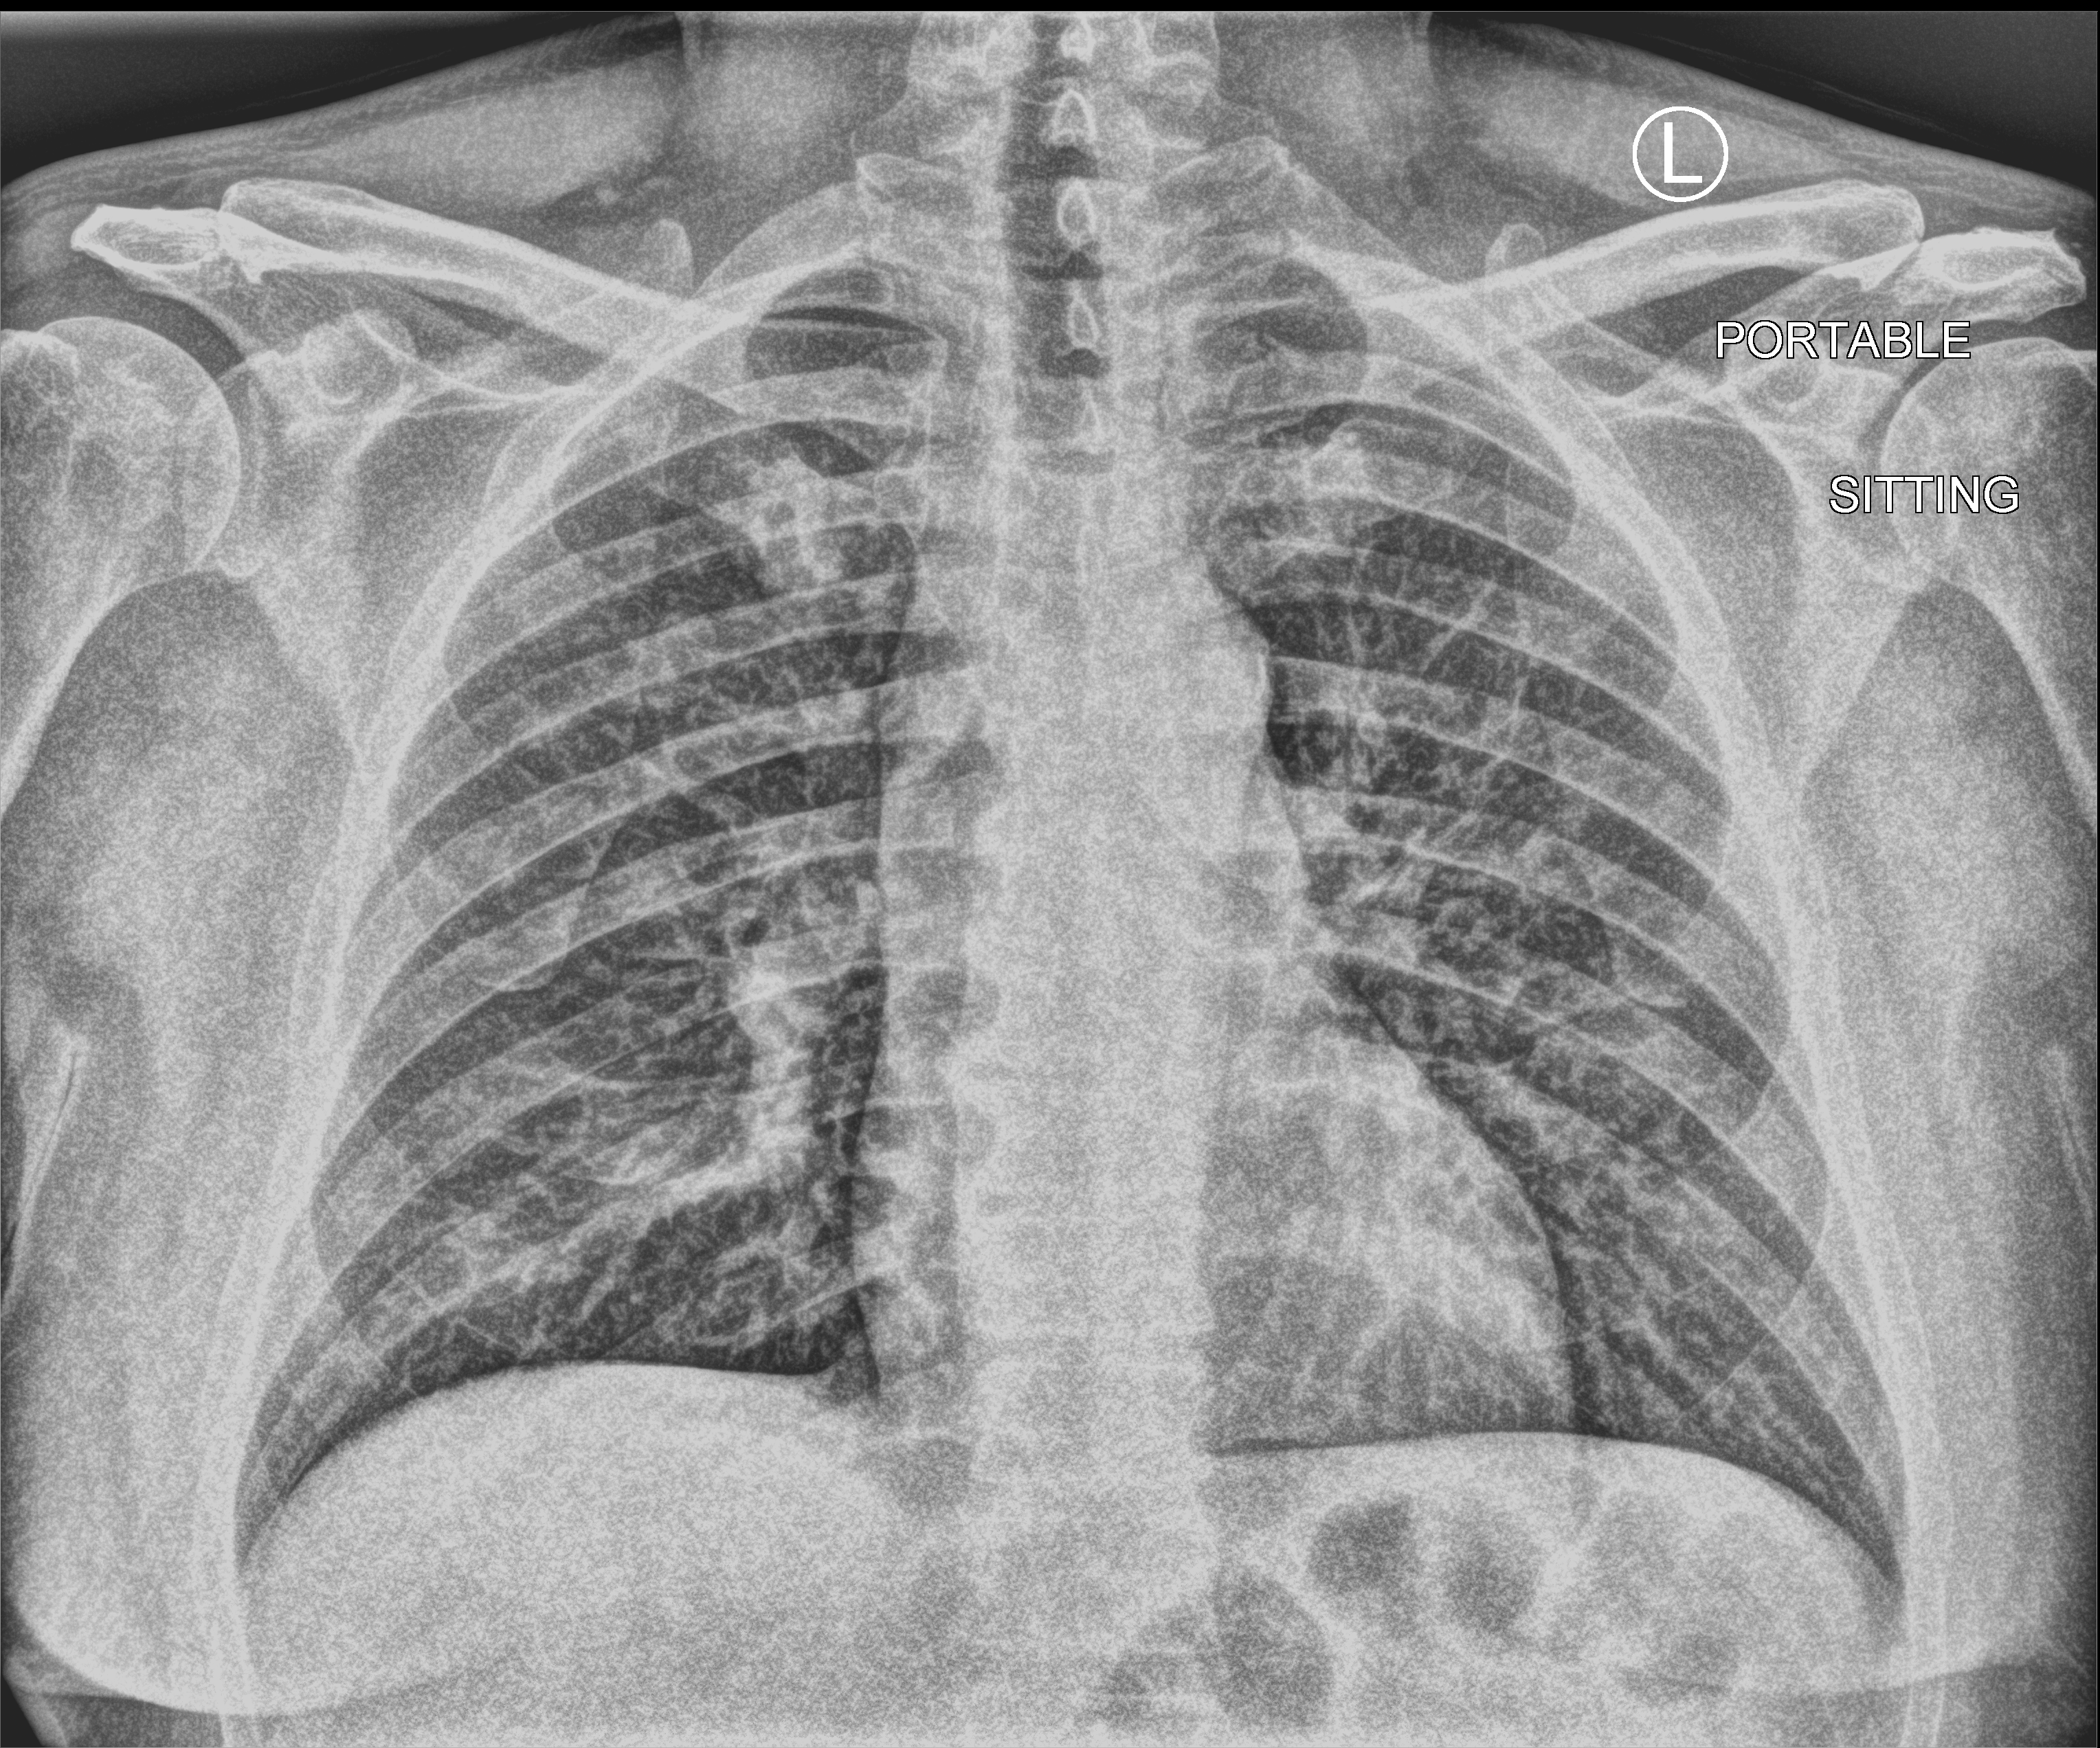
Bedside chest radiograph (computed radiography), anteroposterior (AP) projection. Male patient hospitalised with COVID-19, age 18–59 years.
Hospital-stay facts (about this admission, not read from this image; timing relative to this image not recorded): mechanically ventilated during this hospital stay: no.